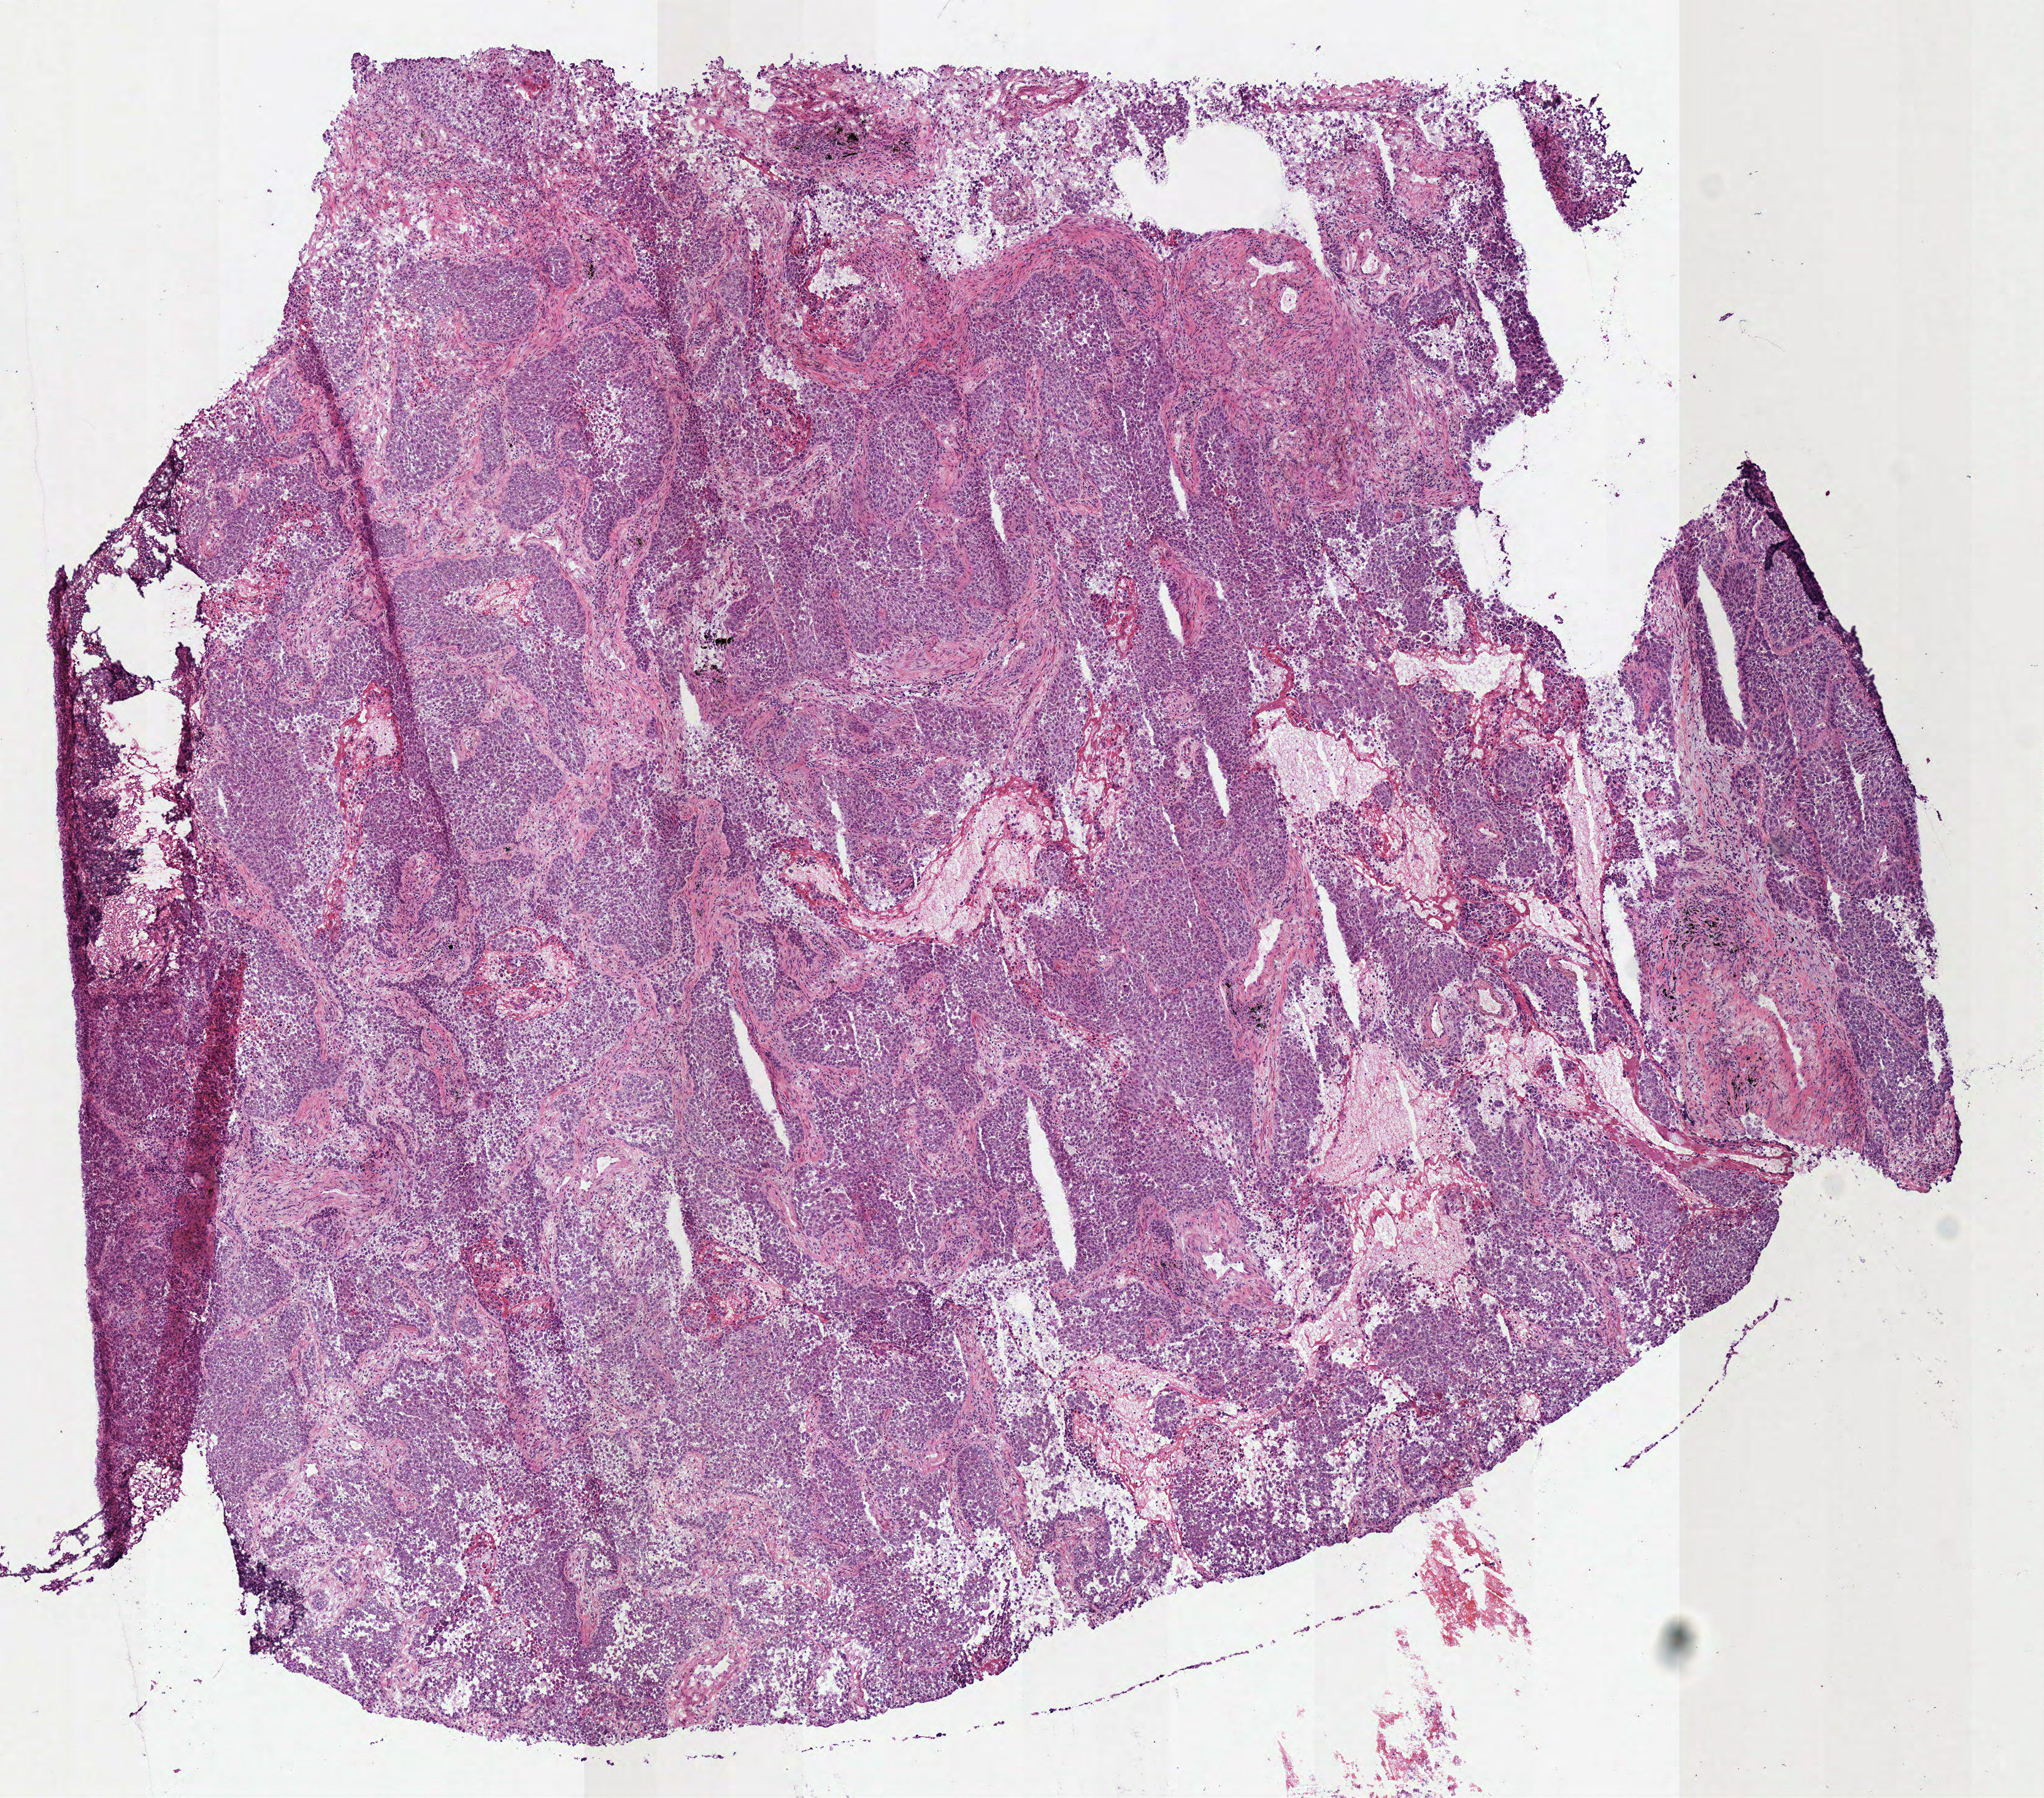
Whole-slide histology image, H&E-stained — whole scanned area (about 6.6 x 5.8 mm, from a 40x scan) shown as a low-resolution overview. Frozen section from the bottom of the tissue portion. Lung, primary tumour sample. Female patient; age at initial diagnosis 72 years. Slide review estimates, as recorded: tumour cells 80%, tumour nuclei 95%, normal cells 0%, stromal cells 18%, necrosis 2%. Infiltration values recorded for this section: lymphocyte infiltration 1%.
* pathologic diagnosis: Squamous cell carcinoma, NOS (upper lobe, lung)
* laterality: right
* AJCC pathologic stage: I